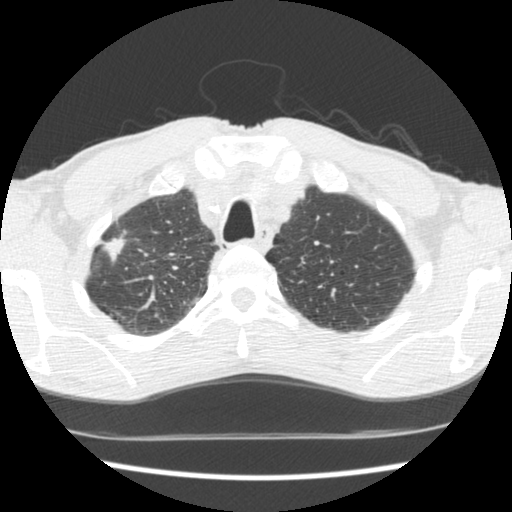
Axial slice from a low-dose chest CT screening exam; baseline screening round; lung window (W 1500 / L -600 HU); slice 36 of 197 in the series; 512 × 512 image matrix, field of view 318 × 318 mm. Male participant, aged 62 years at enrolment. Current smoker at enrolment.
- Lesion marked by an expert reader, bounding box (x1, y1, x2, y2) in pixels: (85, 221, 137, 273).
- No non-calcified nodule or mass ≥4 mm was recorded by the screening reader at this exam.
- Participant outcome: lung cancer diagnosed 640 days after this screen — adenocarcinoma, NOS, right upper lobe, poorly differentiated (G3), stage IIA (AJCC 6th edition), 22 mm at pathology.